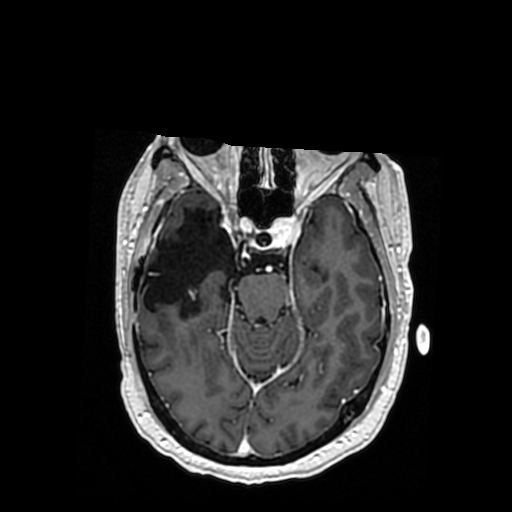
Brain MRI from a brain-tumour surgery series, one axial slice; slice 223 of 364 in the series (ordered by position); T1-weighted post-contrast; 0.5 mm slice thickness; 512 × 512 image matrix. From the clinical record (not read from this slice): histopathology: Oligodendroglioma; WHO grade: 3; IDH mutation: yes.
Structures marked on this image (outlined manually by an expert reader):
- previous resection cavity: bounding box [x1, y1, x2, y2] px = [142, 208, 235, 319]